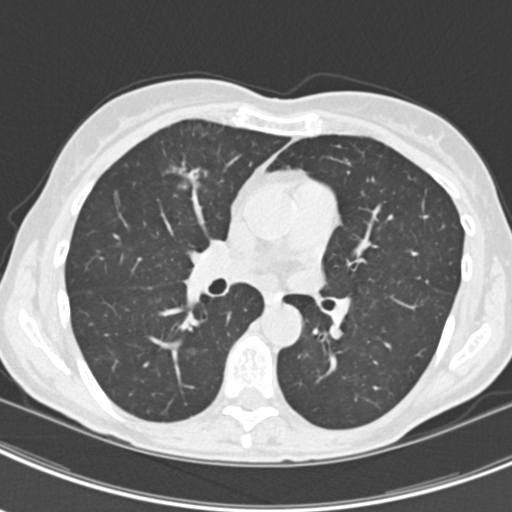
Low-dose screening chest CT, axial slice; second annual screen; lung window (W 1500 / L -600 HU); standard (soft-tissue) reconstruction kernel (B30f); slice 90 of 219 in the series. Female participant, aged 63 years at enrolment. Current smoker at enrolment.
Lesion marked by an expert reader, bounding box [x1, y1, x2, y2] px = [162, 150, 222, 201]. The screening reader recorded 9 non-calcified nodules or masses ≥4 mm on this exam (left upper lobe, right upper lobe, left upper lobe, left lower lobe, right middle lobe, left lower lobe, left lower lobe, right lower lobe, right lower lobe); which of them this box marks is not recorded.